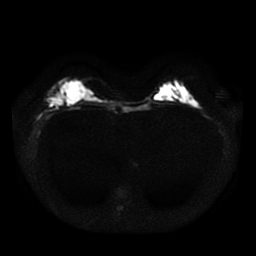
Breast MRI, one axial slice; slice 13 of 41 in the series (ordered by position); diffusion-weighted series; image 2 of 4 stored at this slice position (different b-values; order by instance number); 1.5 T; 256 × 256 image matrix. Female patient.
Structures marked on this image (expert manual segmentation):
- tumour on diffusion-weighted imaging: bounding box (x1, y1, x2, y2) in pixels: (47, 95, 64, 106)